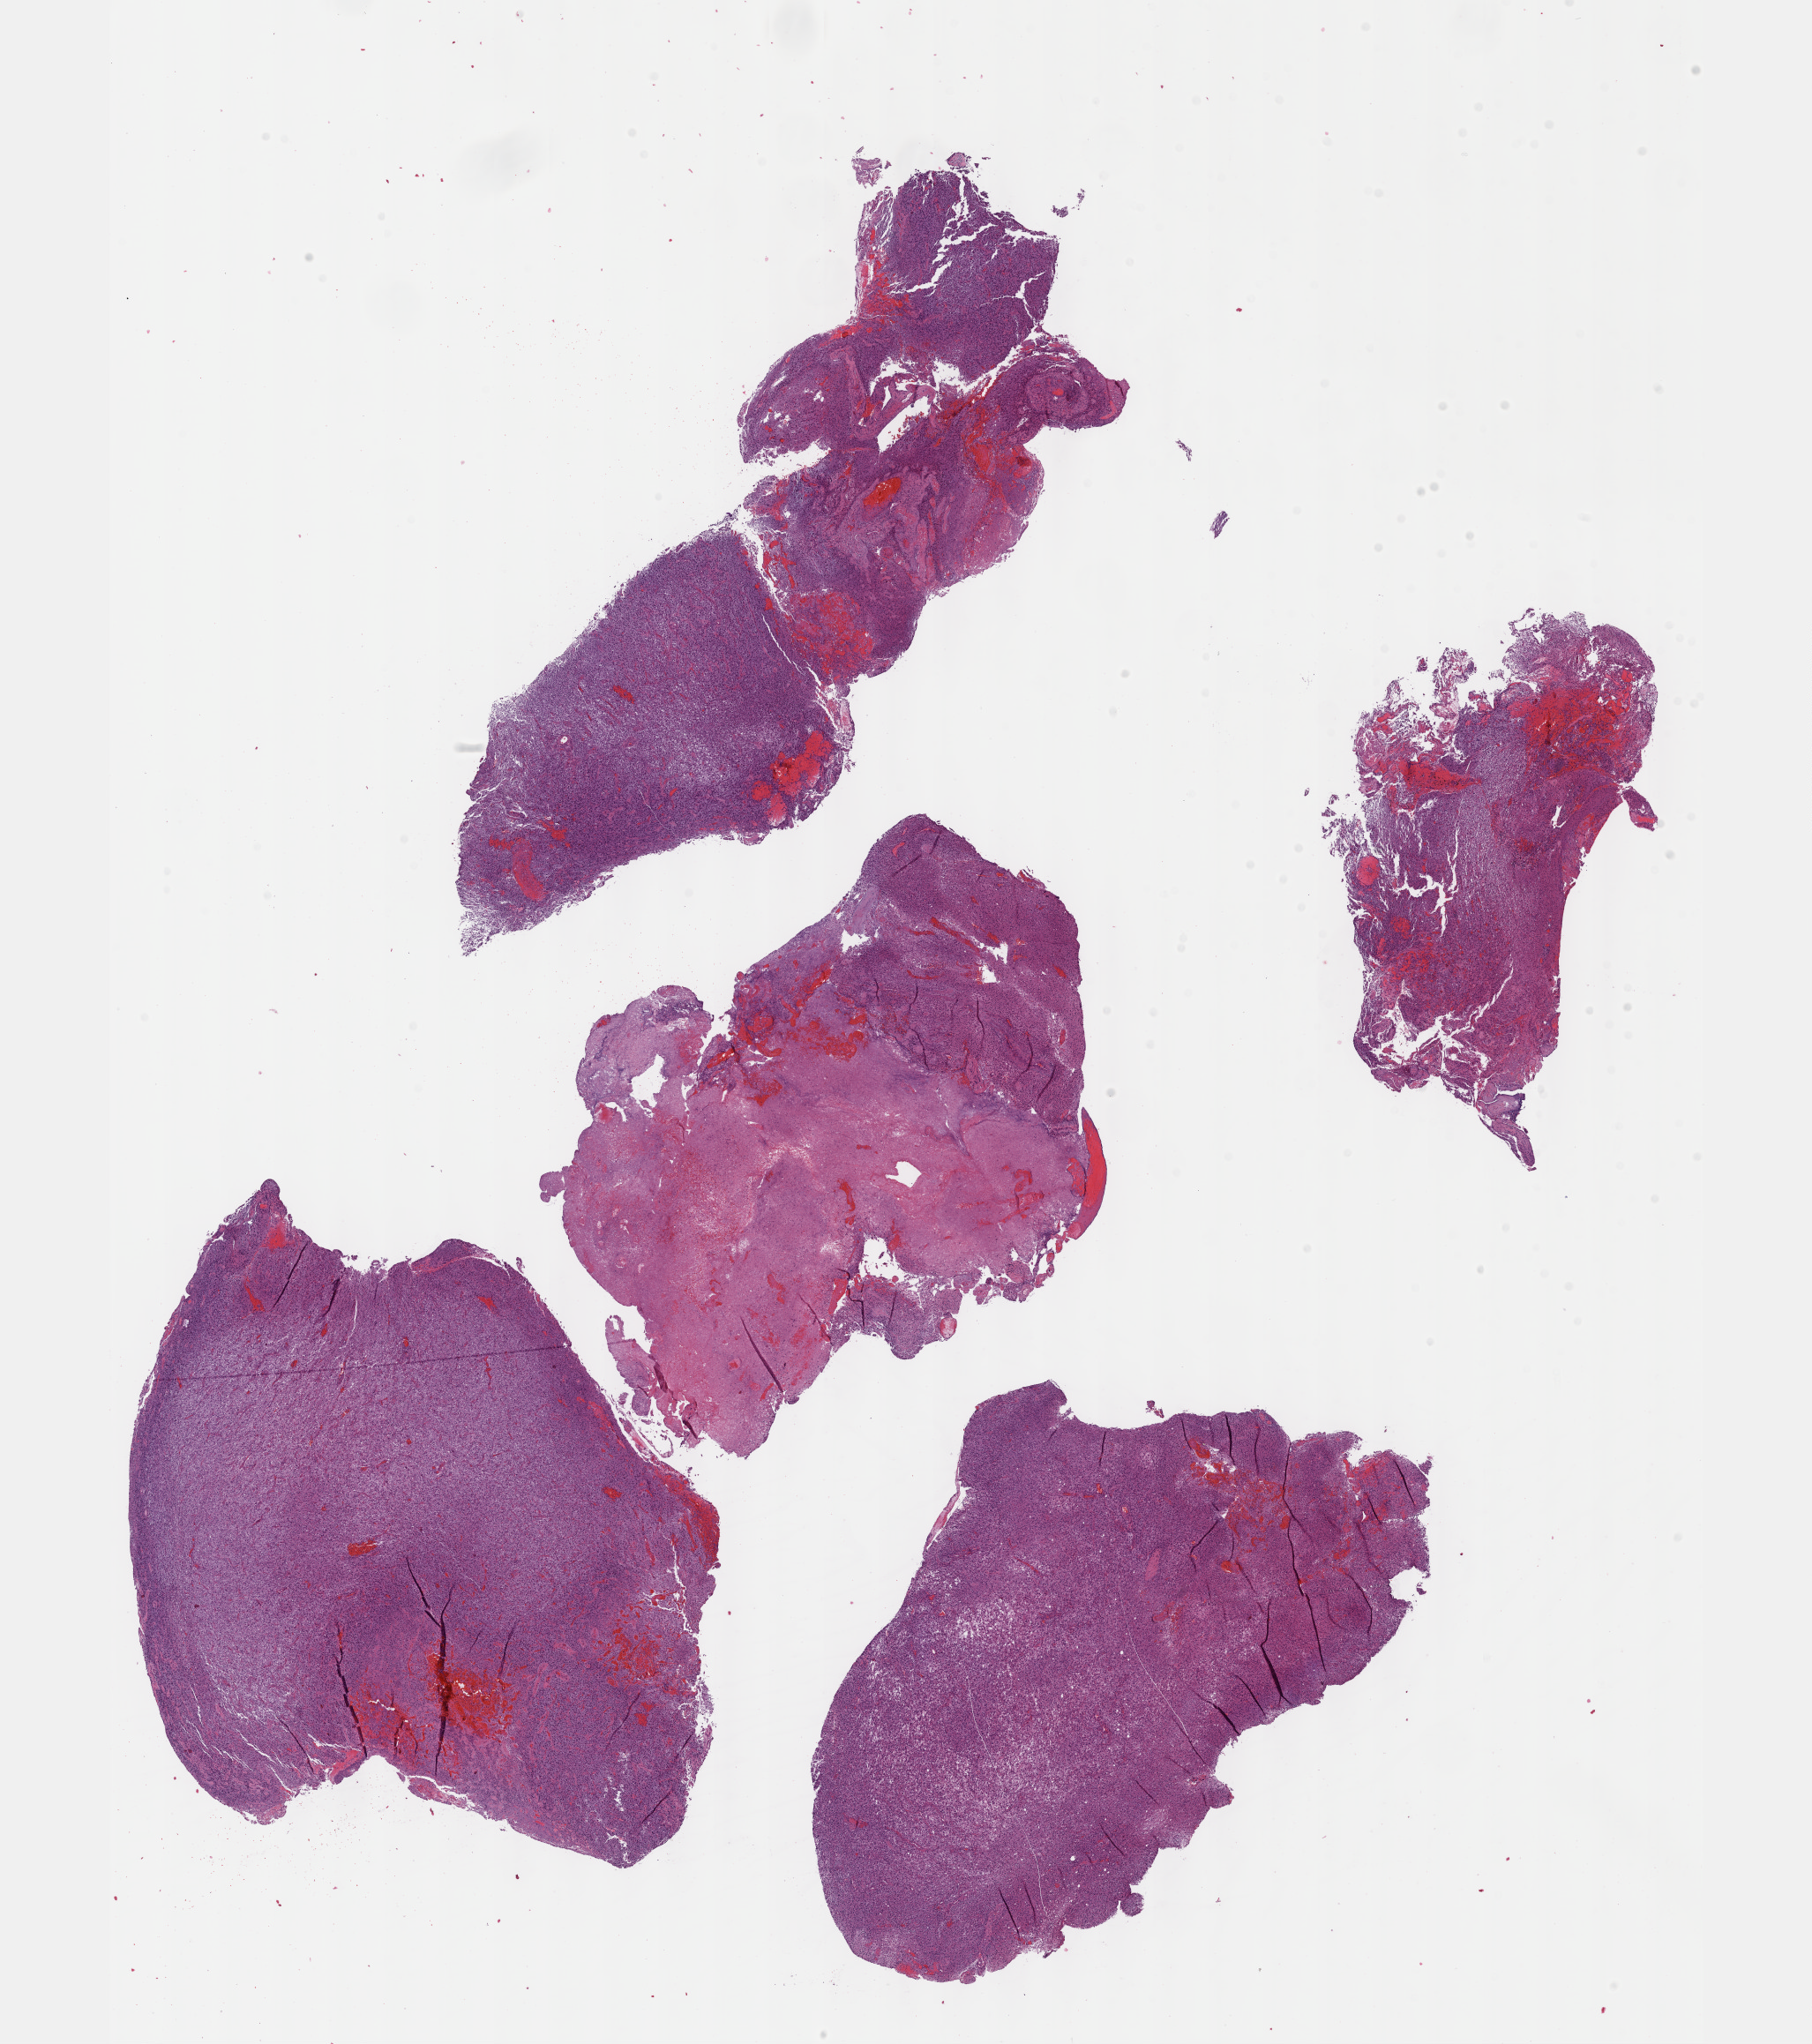
H&E whole-slide image, shown as a low-resolution overview of the whole scanned area (about 16.6 x 18.7 mm, from a 40x scan), formalin-fixed paraffin-embedded (FFPE) diagnostic section, primary tumour sample from the brain. Male, age 66 years at initial diagnosis. Histologic grade: G3 (poorly differentiated).
* pathologic diagnosis: Oligodendroglioma, anaplastic (cerebrum)
* laterality: left